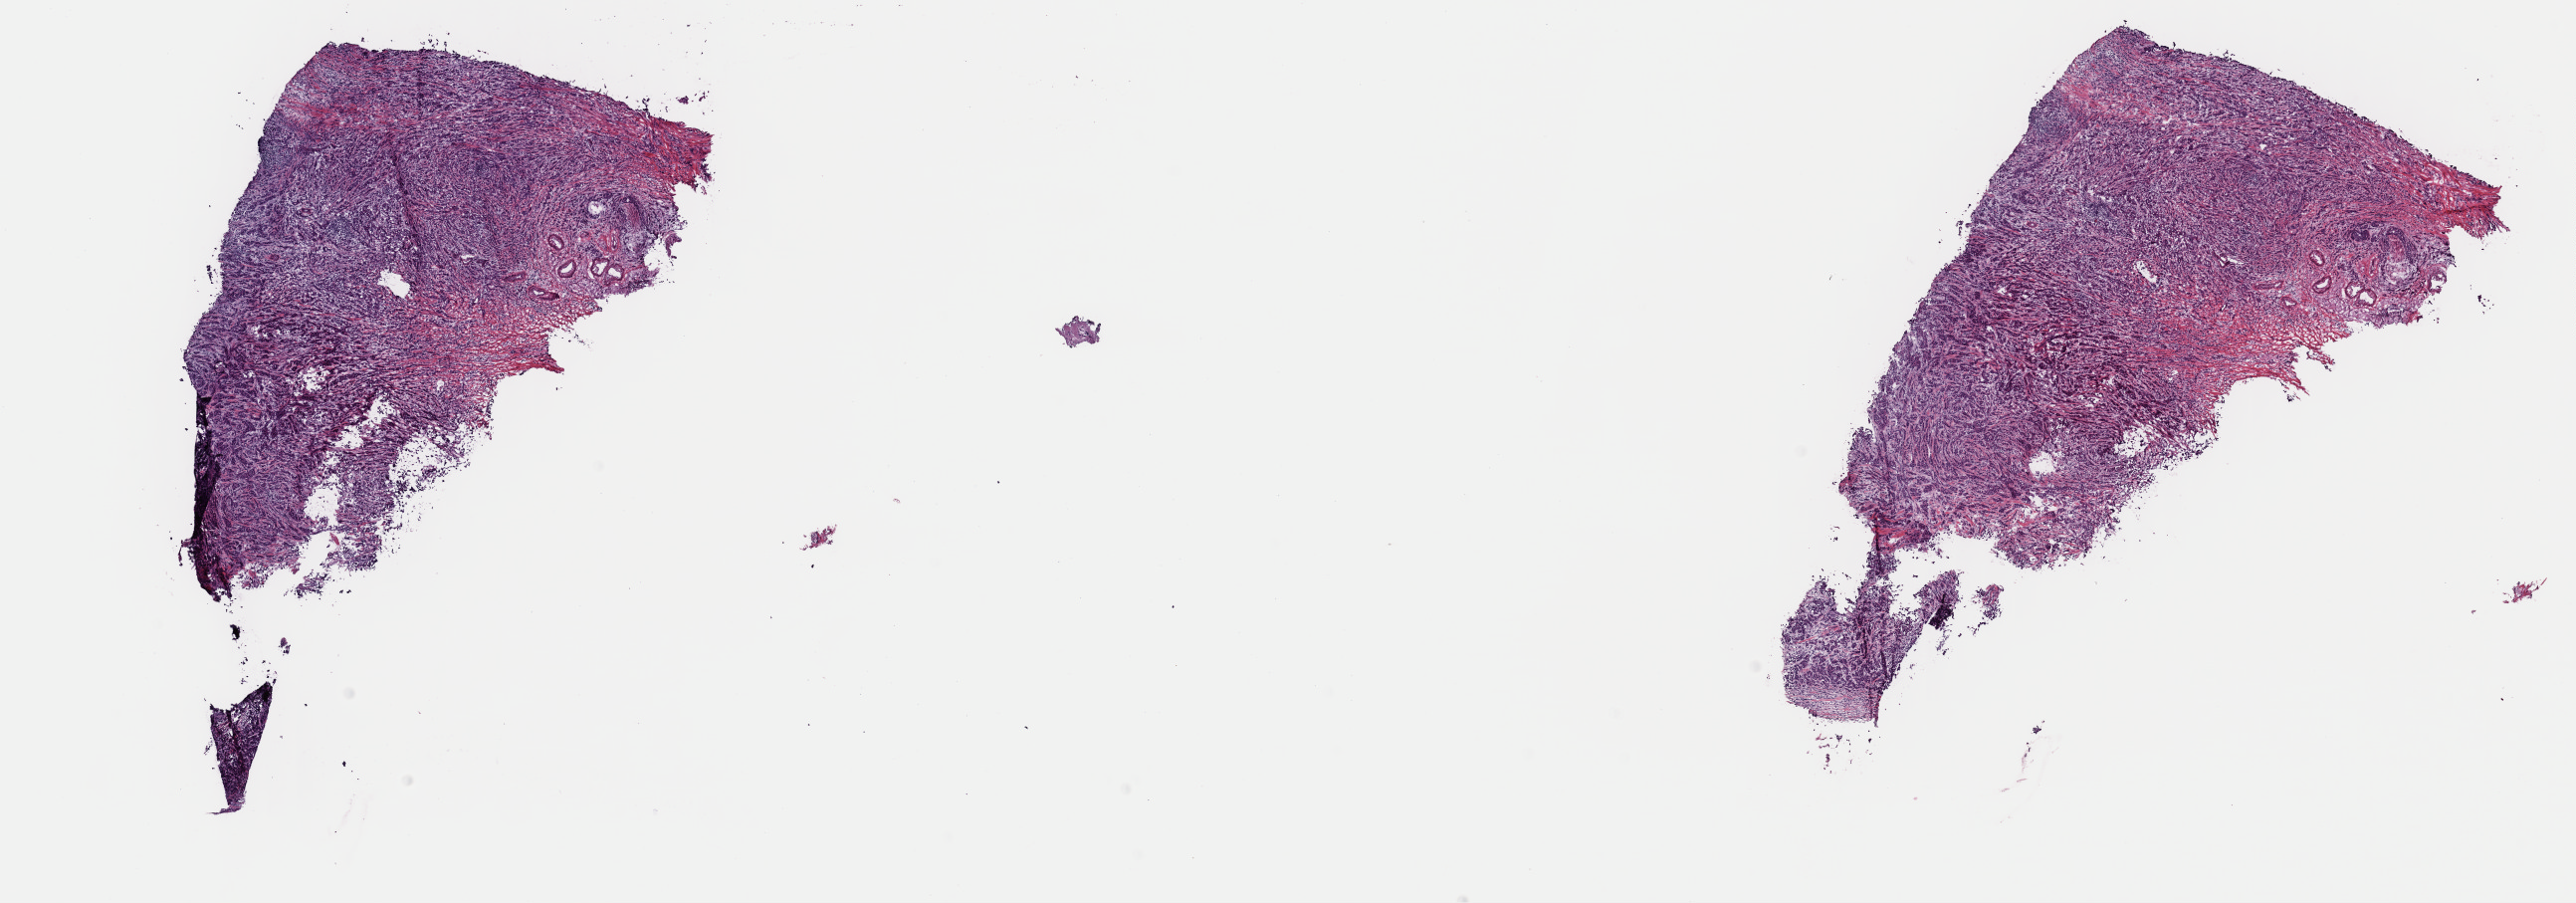
Digitized Hematoxylin and eosin (H&E) stained tissue section (whole slide), whole scanned area (about 20.4 x 7.2 mm) shown as a low-resolution overview, frozen section, sample: primary tumour, breast. Female, age 55 years at initial diagnosis. Composition of this section per pathologist review: tumour cells 75%, tumour nuclei 75%, normal cells 1%, stromal cells 23%, necrosis 1%. Infiltration values recorded for this section: lymphocyte infiltration 4%, monocyte infiltration 2%, neutrophil infiltration 2%.
Diagnosis: Infiltrating duct and lobular carcinoma. AJCC pathologic stage: IIIC (6th edition).